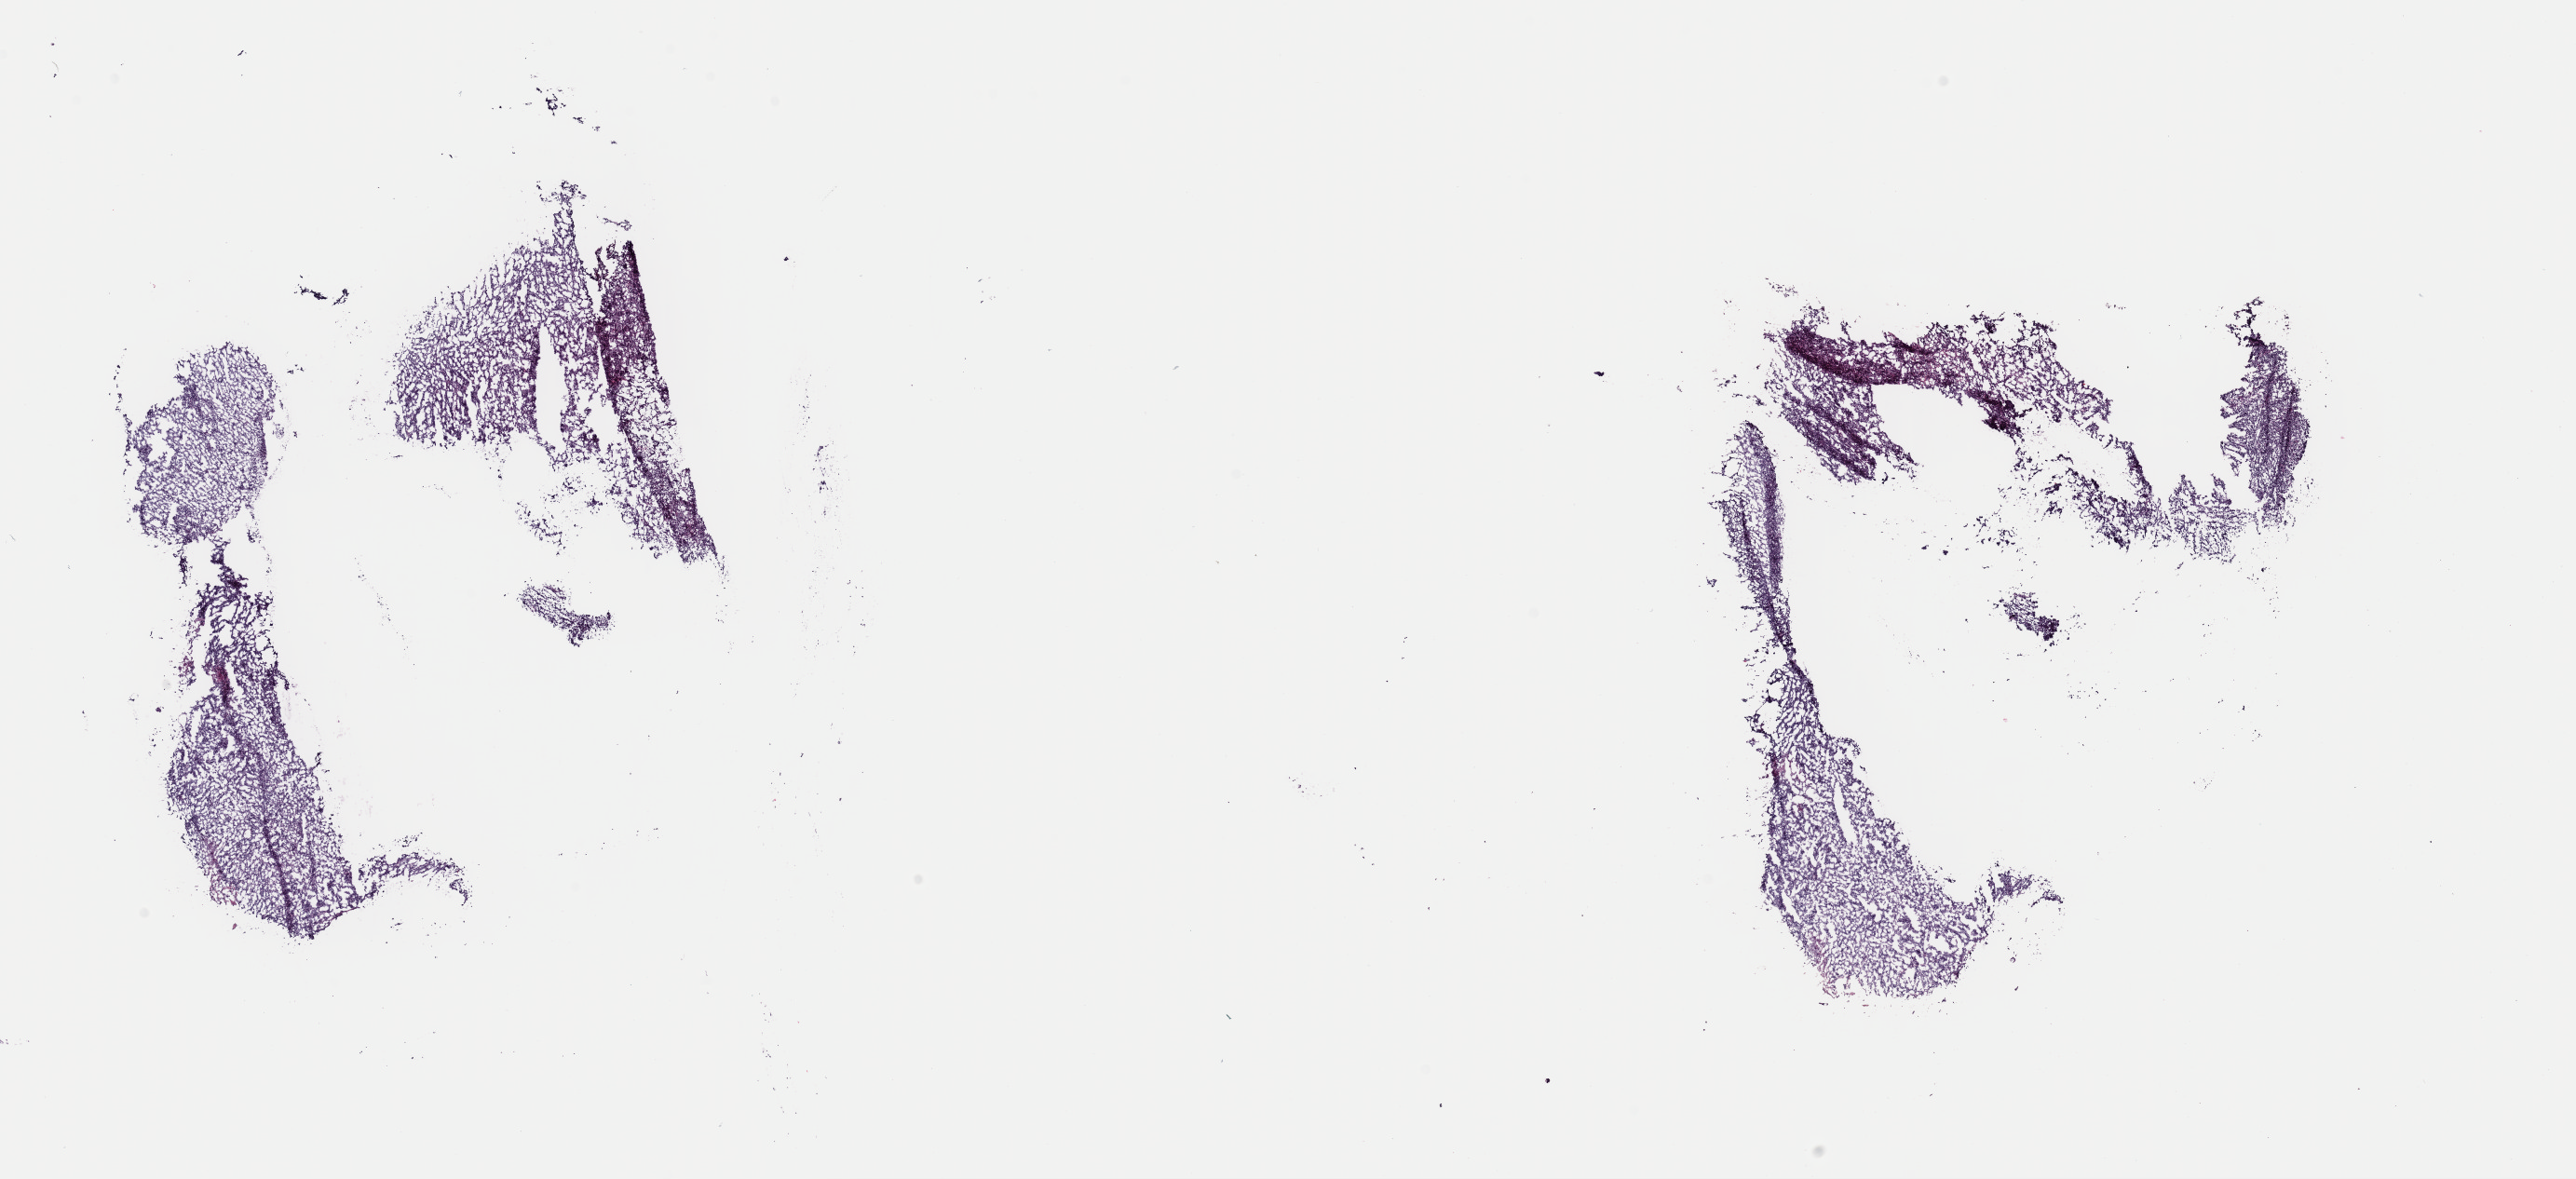
Digitized Hematoxylin and eosin (H&E) stained tissue section (whole slide) — shown as a low-resolution overview of the whole scanned area (about 21.9 x 10.0 mm, slide scanned at 40x). Frozen section from the top of the tissue portion. Sample: primary tumour, uterus. Patient: female, age at initial diagnosis 68 years. Histologic grade: G3 (poorly differentiated). Composition of this section per pathologist review: tumour cells 60%, tumour nuclei 60%, normal cells 10%, stromal cells 20%, necrosis 10%. Inflammatory infiltration, as recorded: lymphocyte infiltration 1%, monocyte infiltration 1%, neutrophil infiltration 2%.
Histologic diagnosis: Serous cystadenocarcinoma, NOS (endometrium). FIGO stage: IA.